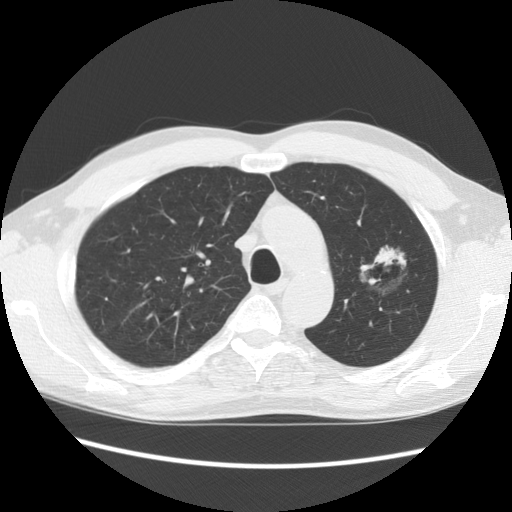
Chest CT (low-dose screening protocol), one axial image; second screening round (one year after baseline); lung window (W 1500 / L -600 HU); standard (soft-tissue) reconstruction kernel (STANDARD); slice 102 of 139 in the series. Male participant, aged 61 years at enrolment. Former smoker at enrolment.
Expert reader's lesion annotation, bounding box (x1, y1, x2, y2) in pixels: (346, 224, 424, 299). Reader record for this screening exam (exam-level; its link to the box is not recorded): non-calcified nodule or mass ≥4 mm, left upper lobe, 34 × 32 mm, poorly defined margins, mixed attenuation, pre-existing on the prior screen: yes; interval growth: no. Participant outcome: lung cancer diagnosed 704 days after this screen (after the third annual screen) — bronchiolo-alveolar adenocarcinoma, NOS, left upper lobe, well differentiated (G1), stage IB (AJCC 6th edition), 44 mm at pathology.